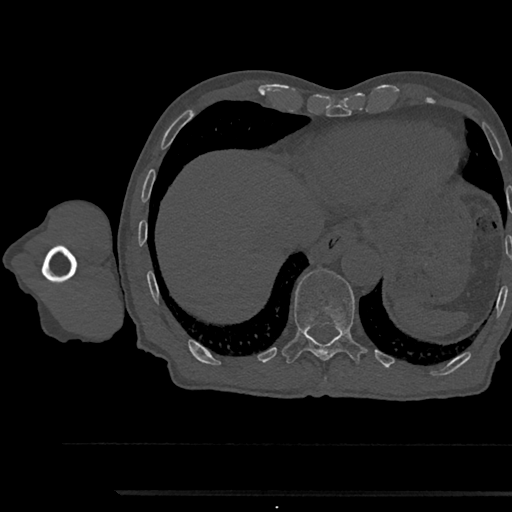
CT including the spine, one axial slice. Slice 792 of 797 in the series (ordered by position). Bone window (W 1800 / L 400 HU). 0.5 mm slice thickness. 512 × 512 image matrix, field of view 367 × 367 mm. Male patient, age 79 years. Case-level facts recorded for this patient, not image findings: primary cancer: prostate.
Outlined on this slice (semi-automatic segmentation, software-assisted and operator-edited):
- T11 vertebra: box from (x=282, y=270) to (x=366, y=363) px